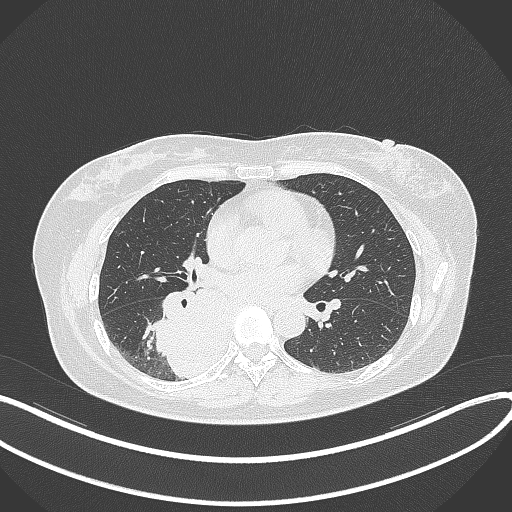
Chest CT, one axial slice; slice 173 of 331 in the series (ordered by position); reconstruction kernel B70f; 120 kVp; lung window (W 1500 / L -600 HU); 512 × 512 image matrix. Patient: female, 54 years. From the clinical record (not read from this slice): clinical TNM (as recorded): T4 N0 M0.
Outlined on this slice (rectangle marked by the reading radiologist):
- lung tumour (recorded histology: adenocarcinoma): bounding box [x1, y1, x2, y2] px = [147, 283, 227, 385]